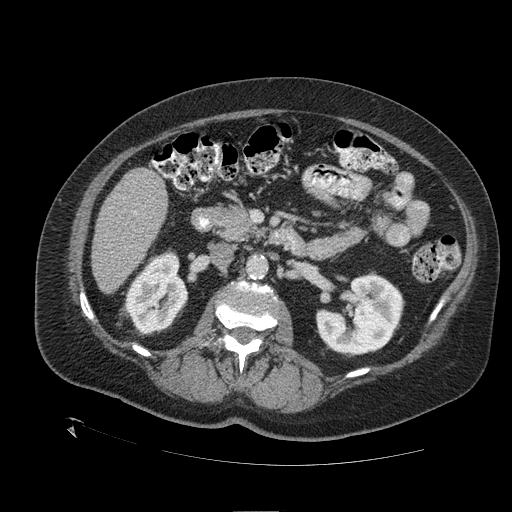
Contrast-enhanced abdominal CT (liver protocol), one axial slice. Slice 47 of 109 in the series (ordered by position). Reconstruction kernel STANDARD. One of 2 acquisitions stored at this slice position. Soft-tissue window (W 400 / L 40 HU). 512 × 512 image matrix. Case-level facts recorded for this patient, not image findings: diagnosis: hepatocellular carcinoma (patient treated with transarterial chemoembolisation; whether this scan precedes or follows treatment is not stated here); TNM stage (as recorded): Stage-I; Child-Pugh class: A; tumour differentiation: no biopsy; tumour nodularity: uninodular.
Structures marked on this image (semi-automatic segmentation, software-assisted and operator-edited):
- liver parenchyma outside the tumour (the mass and vessels are separate outlines, so this box may not span the whole liver): bounding box <92,168,168,293> (left, top, right, bottom; pixels)